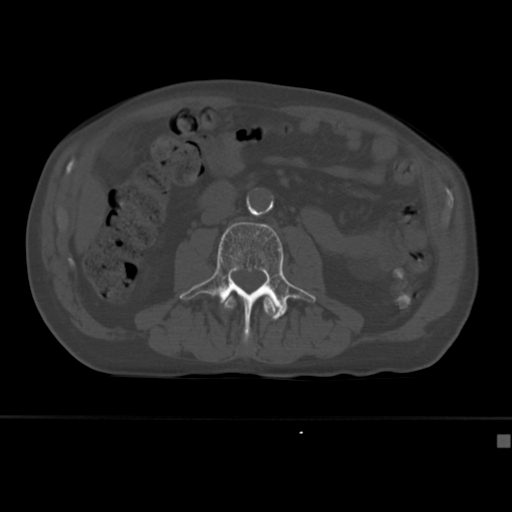
CT including the spine, one axial slice. Position 131 of 430 along the scan axis. 120 kVp. Bone window (W 1800 / L 400 HU). 512 × 512 image matrix. Male patient, age 64 years. Case-level facts recorded for this patient, not image findings: primary cancer: uterus; vertebrae with lytic lesions (as recorded): T1, T4, T5, T7, L5.
Structures marked on this image (semi-automatically segmented with operator editing):
- L2 vertebra: bounding box (x1, y1, x2, y2) in pixels: (223, 296, 278, 317)
- L3 vertebra: (179, 222, 316, 343)